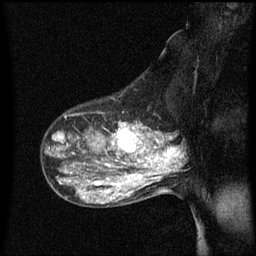
Breast MRI (dynamic contrast-enhanced), one sagittal slice. Dynamic contrast-enhanced series, image 2 of 3 at this slice position (ordered by acquisition). 1.5 T. TE 4.2 ms, TR 8.4 ms. 2 mm slice thickness. 256 × 256 image matrix. Patient: female, 50 years.
Outlined on this slice (semi-automatic segmentation, software-assisted and operator-edited):
- analysis volume of interest (the breast-tissue region the enhancement analysis was run in; not a lesion): box from (x=100, y=114) to (x=153, y=171) px
- tumour enhancement mask (voxels above the 70 % enhancement threshold inside the analysis volume of interest): (x=105, y=124)–(x=153, y=167)